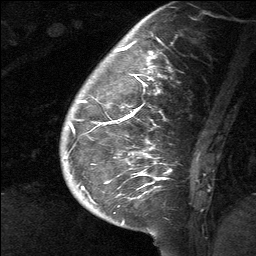
Breast MRI (dynamic contrast-enhanced), one sagittal slice; dynamic contrast-enhanced study with each time point stored as its own series, time point 2 of 3 at this slice position (early post-contrast, ordered by acquisition time); 1.5 T; TE 4.8 ms, TR 27 ms; 2 mm slice thickness; 256 × 256 image matrix, field of view 180 × 180 mm. Female patient, age 39 years. From the clinical record (not read from this slice): setting: breast cancer imaged before/during neoadjuvant chemotherapy; receptor status: HER2-positive.
Structures marked on this image (semi-automatically segmented with operator editing):
- analysis volume of interest (the breast-tissue region the enhancement analysis was run in; not a lesion): box from (x=59, y=40) to (x=201, y=217) px
- tumour enhancement mask (voxels above the 90 % enhancement threshold inside the analysis volume of interest): (x=71, y=42)–(x=171, y=199)